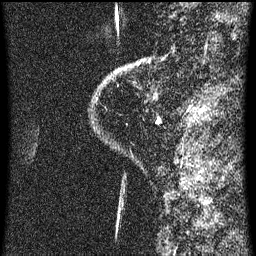
Breast MRI (dynamic contrast-enhanced), one sagittal slice; position 5 of 60 along the scan axis; dynamic contrast-enhanced series, image 2 of 3 at this slice position (ordered by acquisition); 1.5 T; TE 4.2 ms, TR 8 ms; 2 mm slice thickness; 256 × 256 image matrix, field of view 180 × 180 mm. Female patient, age 48 years.
Annotated regions visible in this slice (semi-automatically segmented with operator editing):
- analysis volume of interest (the breast-tissue region the enhancement analysis was run in; not a lesion): bounding box [x1, y1, x2, y2] px = [128, 54, 168, 125]
- tumour enhancement mask (voxels above the 70 % enhancement threshold inside the analysis volume of interest): [149, 62, 161, 123]